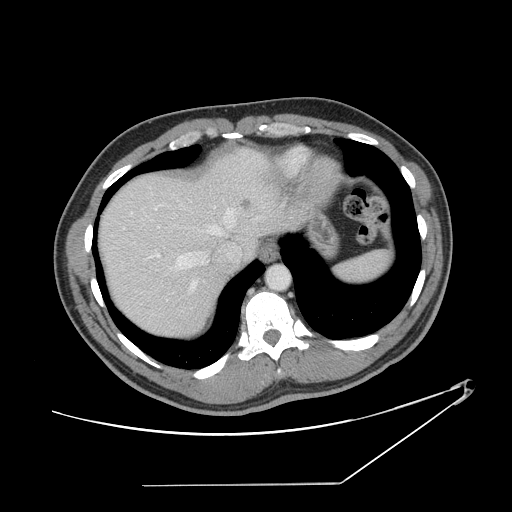
Contrast-enhanced abdominal CT, one axial slice; position 123 of 152 along the scan axis; intravenous contrast given; soft-tissue window (W 400 / L 40 HU); 512 × 512 image matrix, field of view 432 × 432 mm. Male patient, age 45 years. Case-level facts recorded for this patient, not image findings: diagnosis: colorectal cancer liver metastases, imaged before liver resection; multiple liver metastases: no; largest metastasis: 1 cm; disease in both lobes: no.
Outlined on this slice (manually delineated by an expert):
- hepatic veins: bounding box (x1, y1, x2, y2) in pixels: (122, 204, 236, 292)
- liver: (101, 151, 289, 337)
- planned liver remnant (the part of the liver to remain after resection): (102, 176, 234, 337)
- portal vein (with intrahepatic branches): (156, 254, 160, 257)
- liver metastasis: (241, 198, 253, 209)